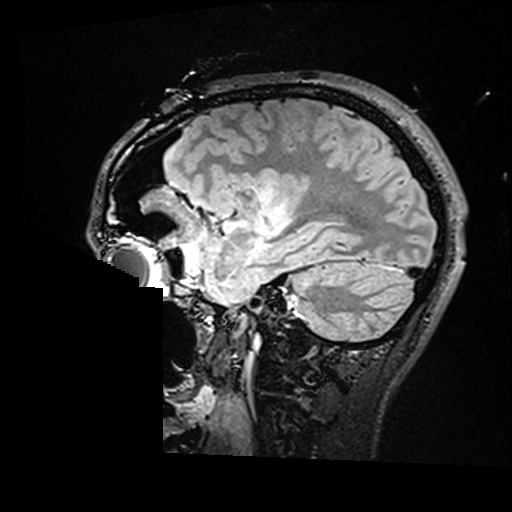
Brain MRI from a brain-tumour surgery series, one sagittal slice. Slice 116 of 176 in the series (ordered by position). T2 FLAIR. 512 × 512 image matrix, field of view 250 × 250 mm. Case-level facts recorded for this patient, not image findings: histopathology: Astrocytoma; WHO grade: 2; IDH mutation: yes; tumour location: Right Insular.
Outlined on this slice (manually delineated by an expert):
- residual tumour: box from (x=260, y=186) to (x=288, y=229) px